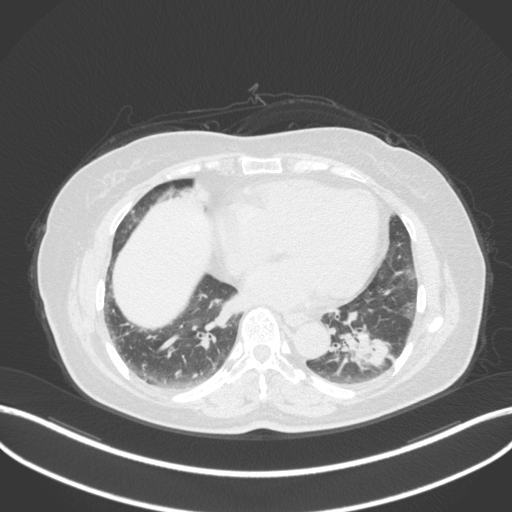
Chest CT, one axial slice. Slice 141 of 307 in the series (ordered by position). 120 kVp. Lung window (W 1500 / L -600 HU). 1 mm slice thickness. 512 × 512 image matrix, field of view 400 × 400 mm. Patient: female, 59 years. Case-level facts recorded for this patient, not image findings: clinical TNM (as recorded): T2a N0 M0; histopathological grade: G2-3.
Structures marked on this image (bounding box drawn by a radiologist):
- lung tumour (recorded histology: adenocarcinoma): bounding box (x1, y1, x2, y2) in pixels: (336, 325, 396, 371)